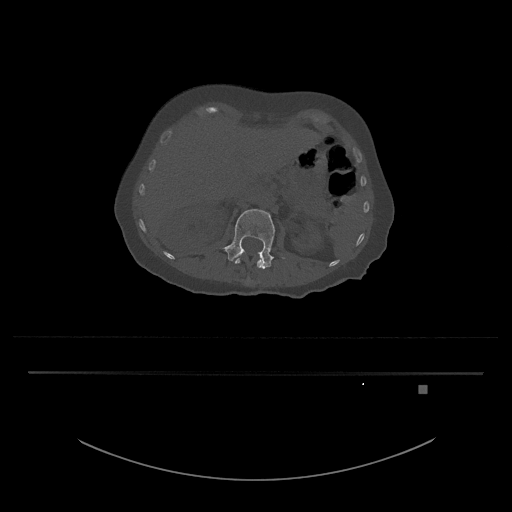
CT including the spine, one axial slice. Position 509 of 797 along the scan axis. 120 kVp. Bone window (W 1800 / L 400 HU). 0.5 mm slice thickness. 512 × 512 image matrix, field of view 500 × 500 mm. Patient: female, 57 years. From the clinical record (not read from this slice): primary cancer: cervical.
Structures marked on this image (semi-automatic segmentation, software-assisted and operator-edited):
- L1 vertebra: bounding box <235,252,265,268> (left, top, right, bottom; pixels)